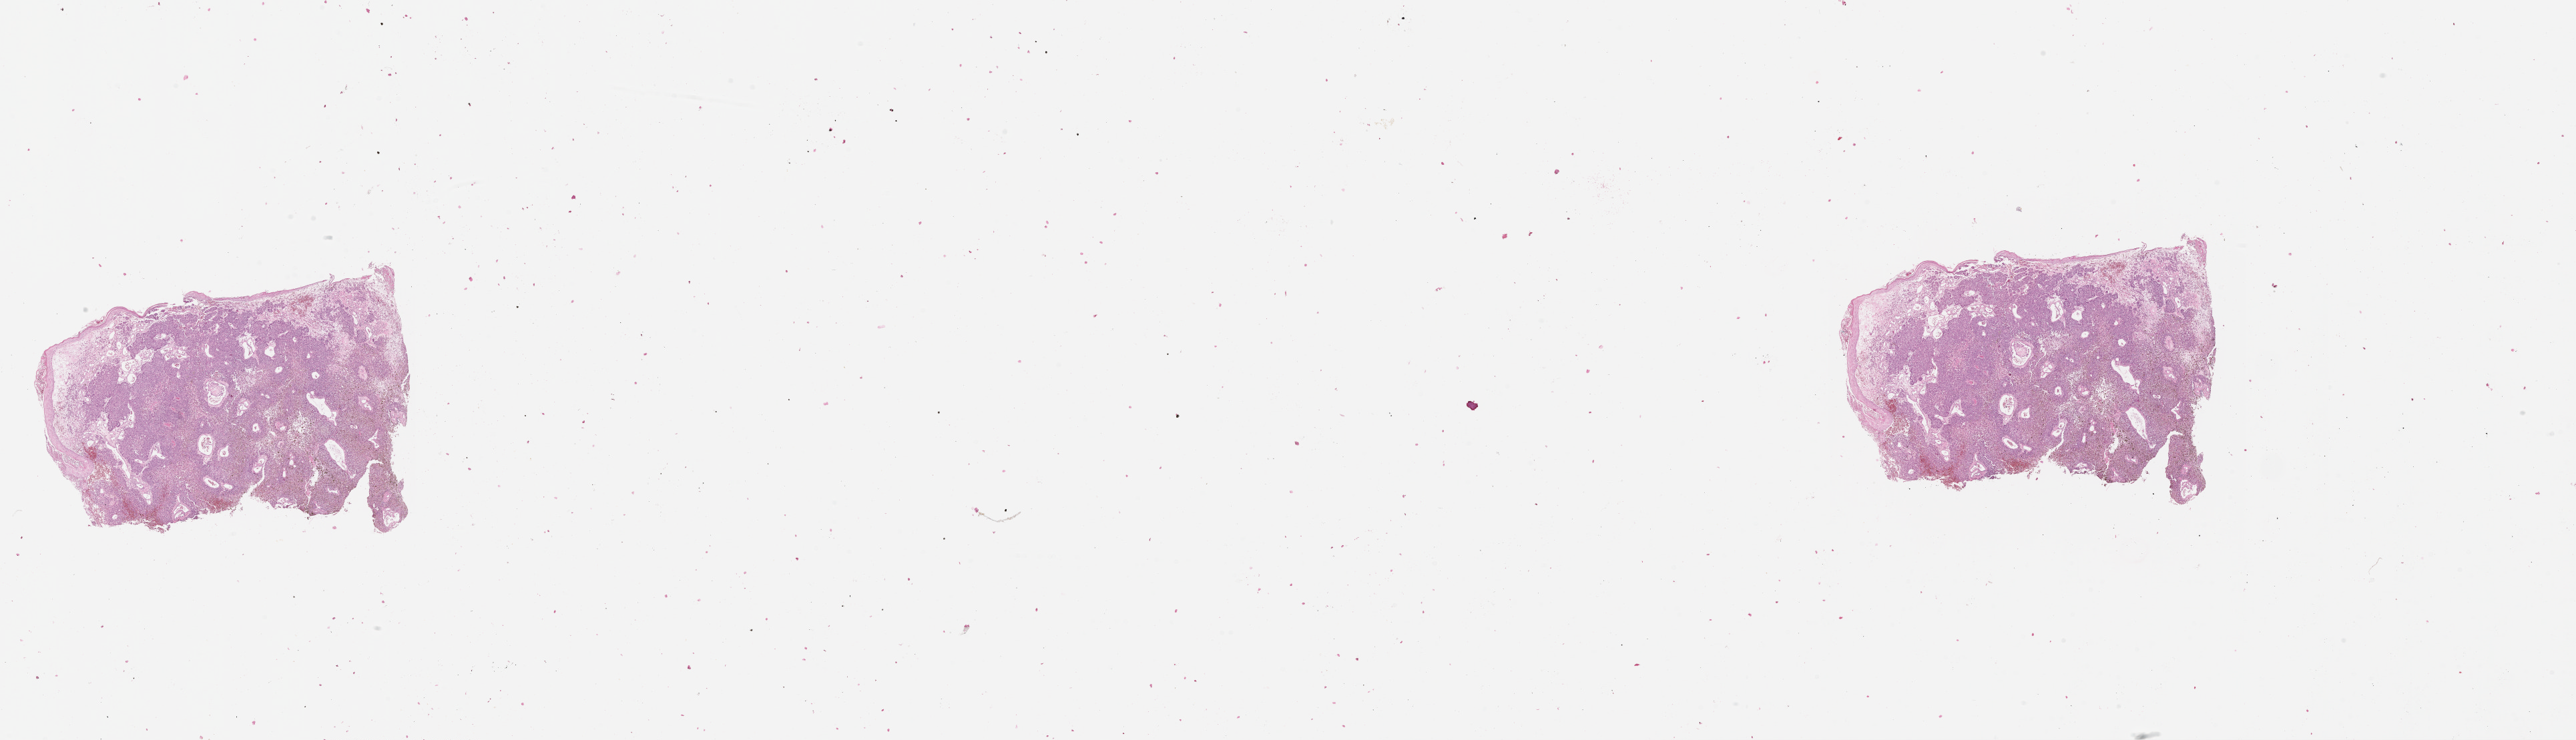
Digitized Hematoxylin and eosin (H&E) stained tissue section (whole slide) — whole scanned area (about 31.1 x 8.9 mm) shown as a low-resolution overview; tumour tissue sample, sampled site: trunk. 61-year-old male patient.
Diagnosis: Malignant melanoma, NOS.